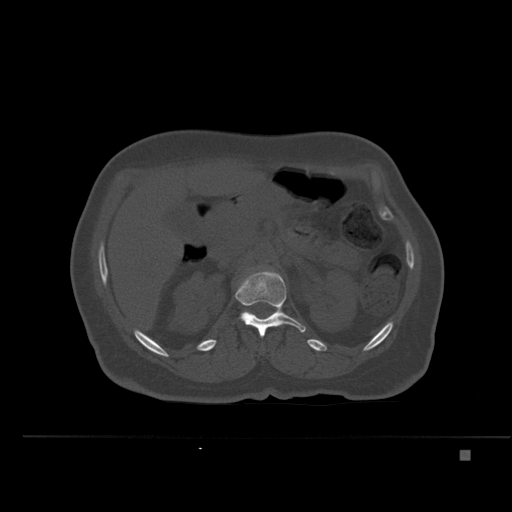
CT including the spine, one axial slice; slice 234 of 477 in the series (ordered by position); bone window (W 1800 / L 400 HU); 512 × 512 image matrix, field of view 422 × 422 mm. Patient: female, 74 years. From the clinical record (not read from this slice): primary cancer: colon.
Structures marked on this image (semi-automatically segmented with operator editing):
- L1 vertebra: bounding box [x1, y1, x2, y2] px = [235, 271, 306, 337]